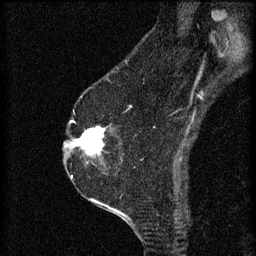
Breast MRI (dynamic contrast-enhanced), one sagittal slice; position 42 of 60 along the scan axis; 3 images stored at this slice position (order not interpretable as contrast timing); 1.5 T; TE 4.2 ms, TR 8.2 ms; 256 × 256 image matrix, field of view 180 × 180 mm. Female patient, age 60 years.
Outlined on this slice (semi-automatic segmentation, software-assisted and operator-edited):
- analysis volume of interest (the breast-tissue region the enhancement analysis was run in; not a lesion): box from (x=74, y=124) to (x=113, y=159) px
- tumour enhancement mask (voxels above the 70 % enhancement threshold inside the analysis volume of interest): (x=74, y=126)–(x=105, y=155)